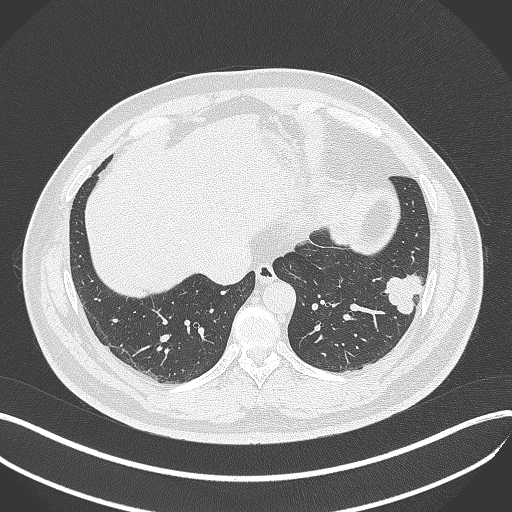
Chest CT, one axial slice. Slice 122 of 429 in the series (ordered by position). Reconstruction kernel B70f. Lung window (W 1500 / L -600 HU). 1 mm slice thickness. 512 × 512 image matrix, field of view 400 × 400 mm. Patient: male, 39 years. From the clinical record (not read from this slice): clinical TNM (as recorded): T2a N0 M0; histopathological grade: G2-3.
Outlined on this slice (bounding box drawn by a radiologist):
- lung tumour (recorded histology: adenocarcinoma): bounding box [x1, y1, x2, y2] px = [383, 269, 431, 320]